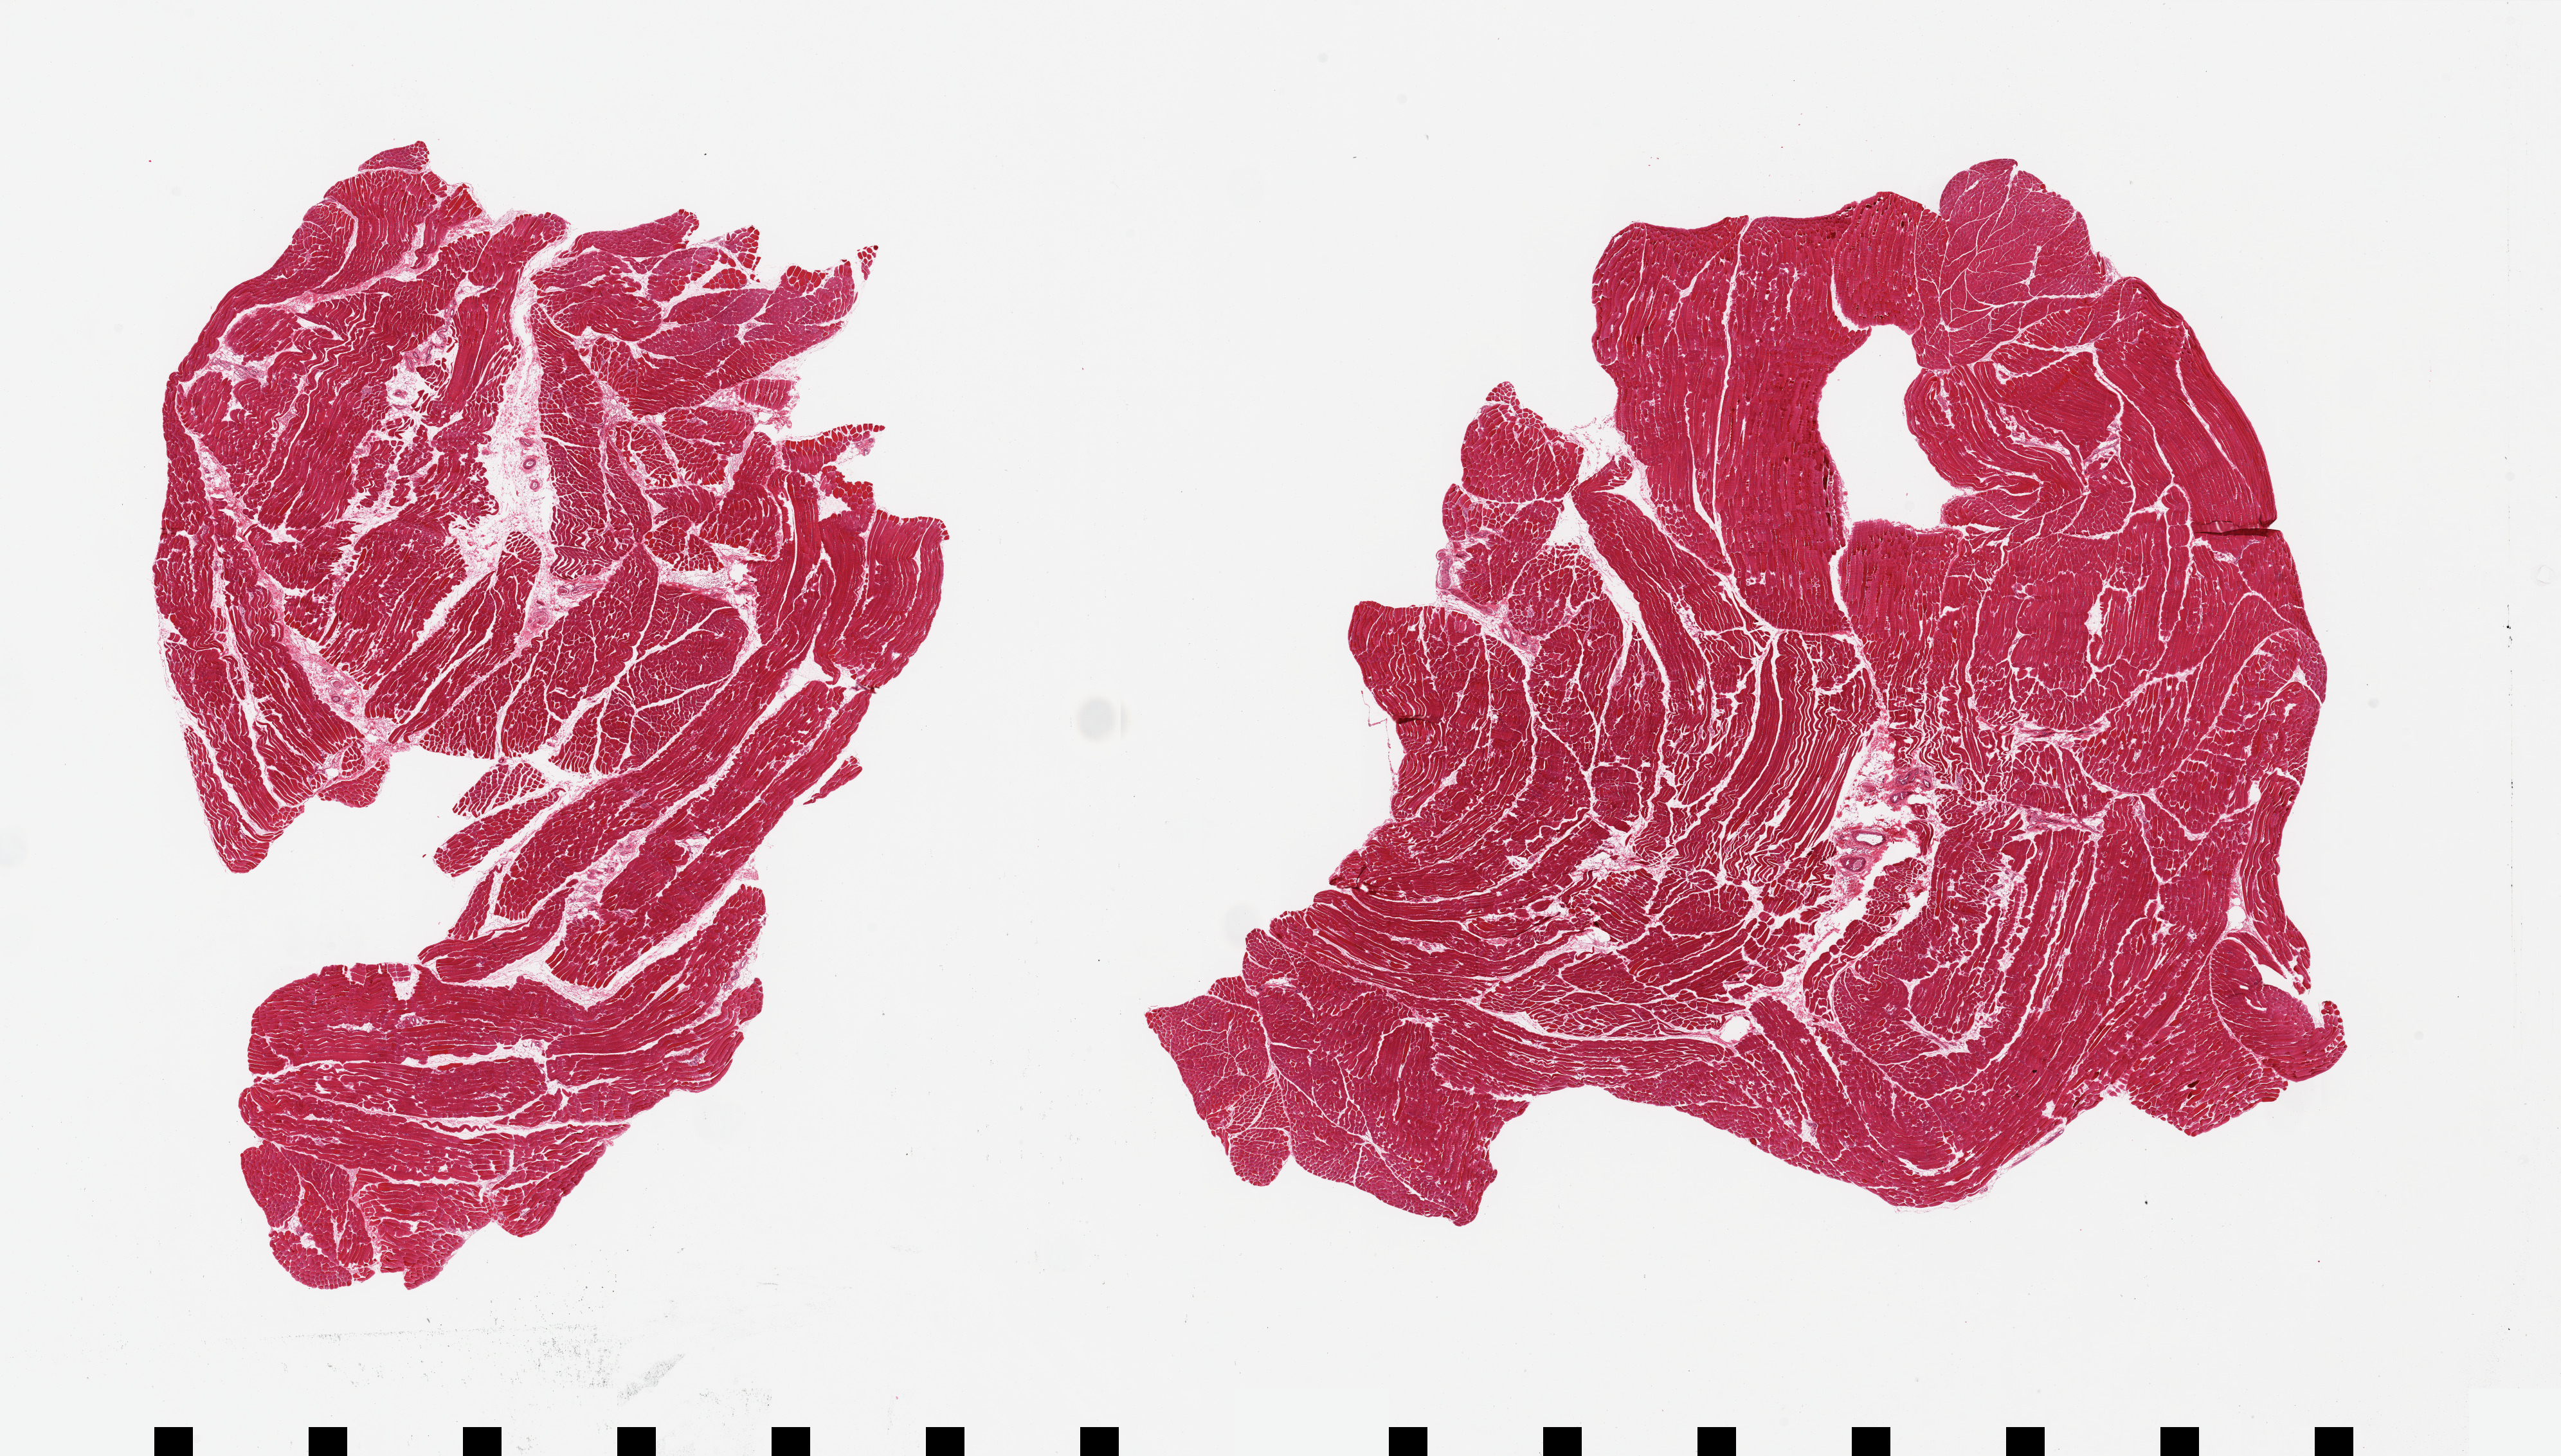
Digitized hematoxylin and eosin (H&E)-stained section, brightfield, a low-resolution overview of the entire scanned area, about 31.5 x 17.9 mm. PAXgene-fixed, paraffin-embedded tissue. Sampled site (target tissue): skeletal muscle. Donor tissue sample.
Reviewer comment on this tissue sample: 2 pieces, !0% interstitial fat.